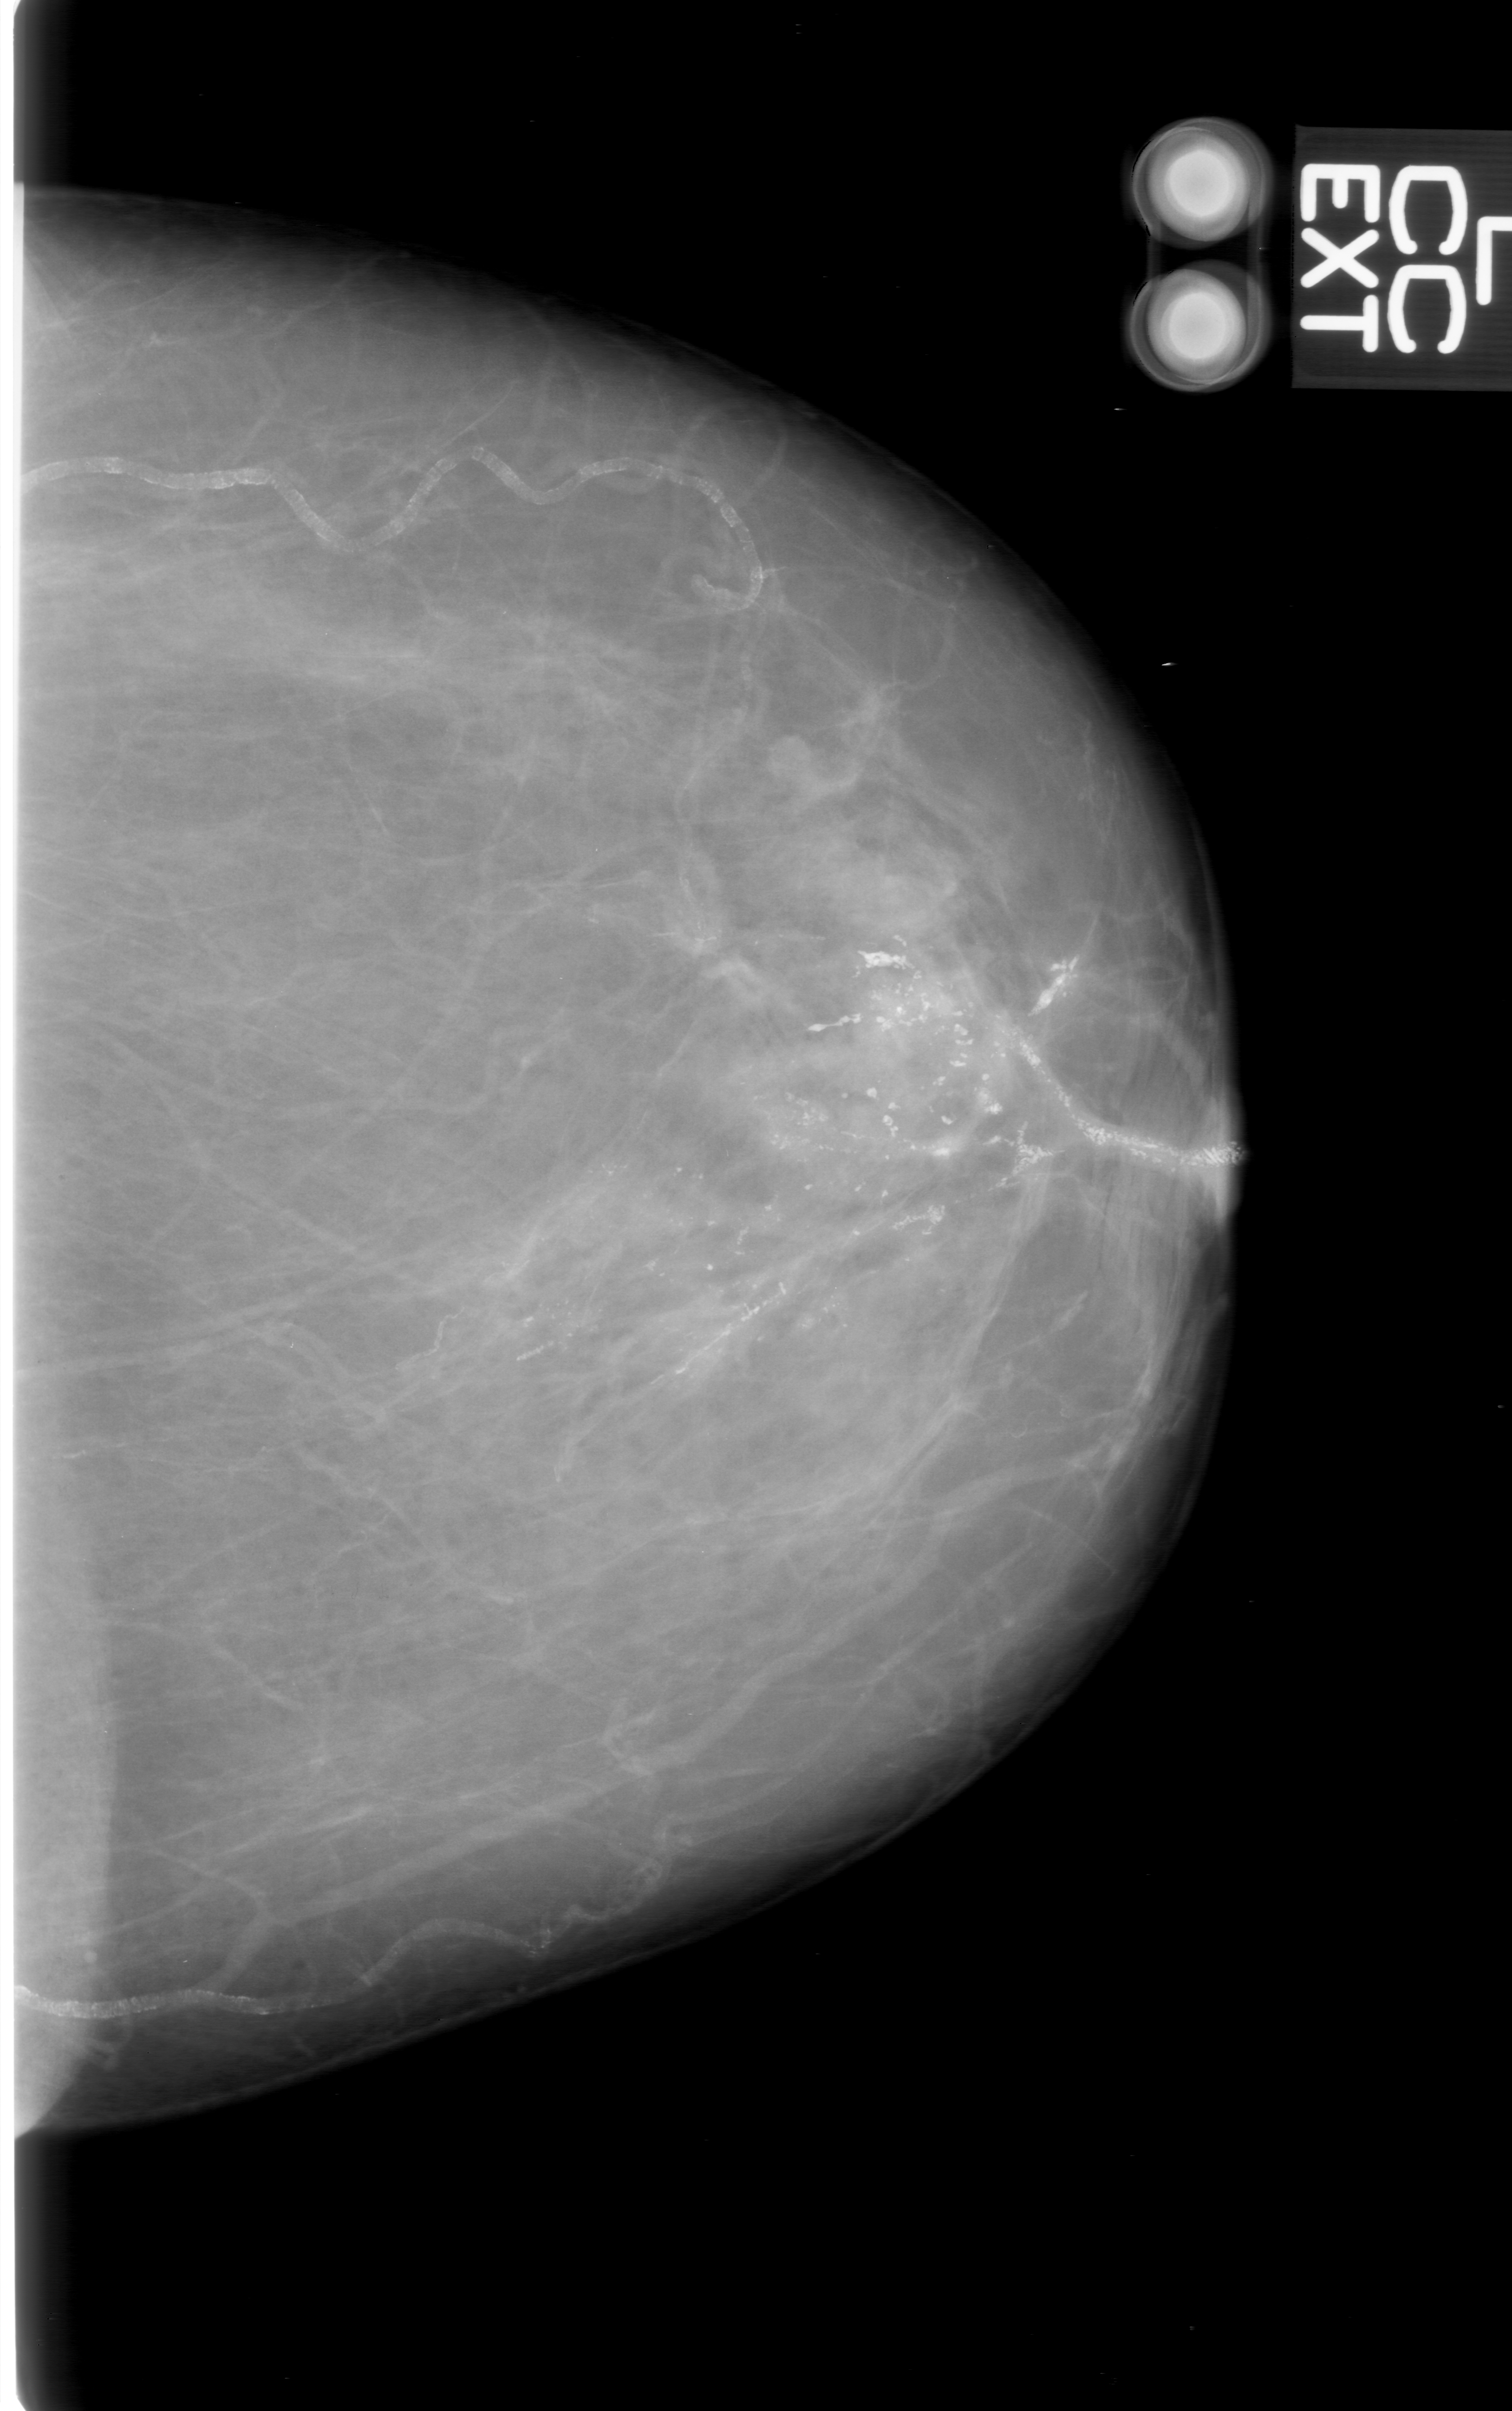
Scanned film-screen mammogram; left breast; craniocaudal (CC) view; breast composition: almost entirely fatty (BI-RADS density category 1 of 4); 1512 × 2411 image matrix.
Marked abnormalities (boxes around the expert regions of interest):
- calcifications, morphology pleomorphic, distribution linear; BI-RADS assessment category 5; pathology result (as recorded, not read from the image): malignant: bounding box (x1, y1, x2, y2) in pixels: (359, 821, 1220, 1562)